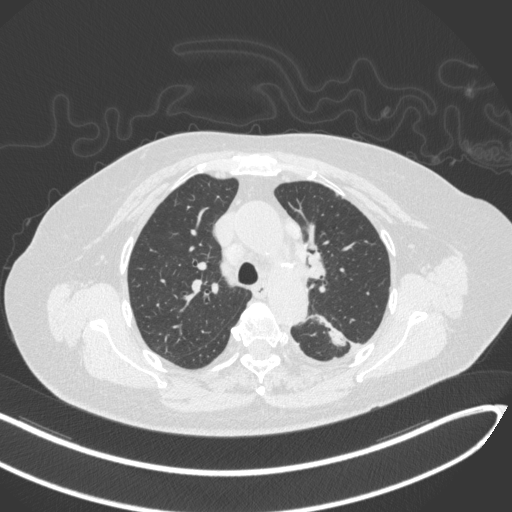
Chest CT, one axial slice; reconstruction kernel B31f; 120 kVp; lung window (W 1500 / L -600 HU); 512 × 512 image matrix, field of view 400 × 400 mm. Patient: female, 76 years. Case-level facts recorded for this patient, not image findings: clinical TNM (as recorded): T1c N0 M0.
Annotated regions visible in this slice (bounding box drawn by a radiologist):
- lung tumour (recorded histology: adenocarcinoma): bounding box [x1, y1, x2, y2] px = [312, 309, 348, 347]